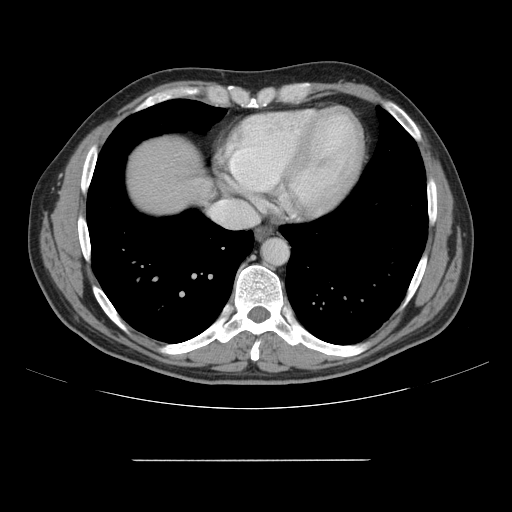
Contrast-enhanced abdominal CT, one axial slice. Slice 147 of 164 in the series (ordered by position). Soft-tissue window (W 400 / L 40 HU). 512 × 512 image matrix, field of view 404 × 404 mm. Male patient, age 54 years. Case-level facts recorded for this patient, not image findings: diagnosis: colorectal cancer liver metastases, imaged before liver resection; multiple liver metastases: yes; largest metastasis: 1 cm; disease in both lobes: no.
Outlined on this slice (outlined manually by an expert reader):
- hepatic veins: bounding box <210,200,258,224> (left, top, right, bottom; pixels)
- liver: <128,138,209,213>
- planned liver remnant (the part of the liver to remain after resection): <128,137,210,212>